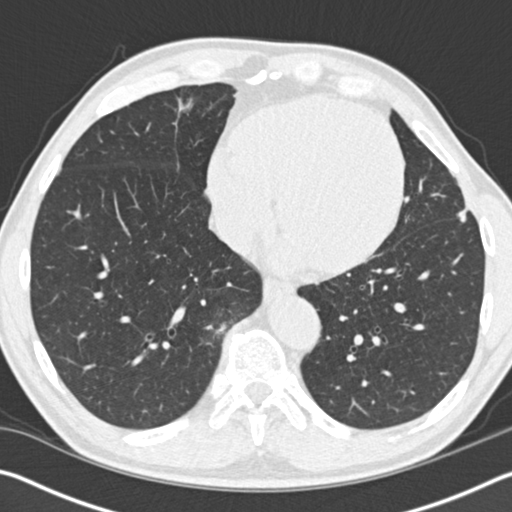
Low-dose screening chest CT, one axial slice; slice 49 of 162 in the series (ordered by position); reconstruction kernel B30f; 120 kVp; lung window (W 1500 / L -600 HU); 512 × 512 image matrix, field of view 340 × 340 mm.
Structures marked on this image (outlined manually by an expert reader):
- lesion 1 (tumor, upper lobe of left lung): bounding box <457,208,468,223> (left, top, right, bottom; pixels)